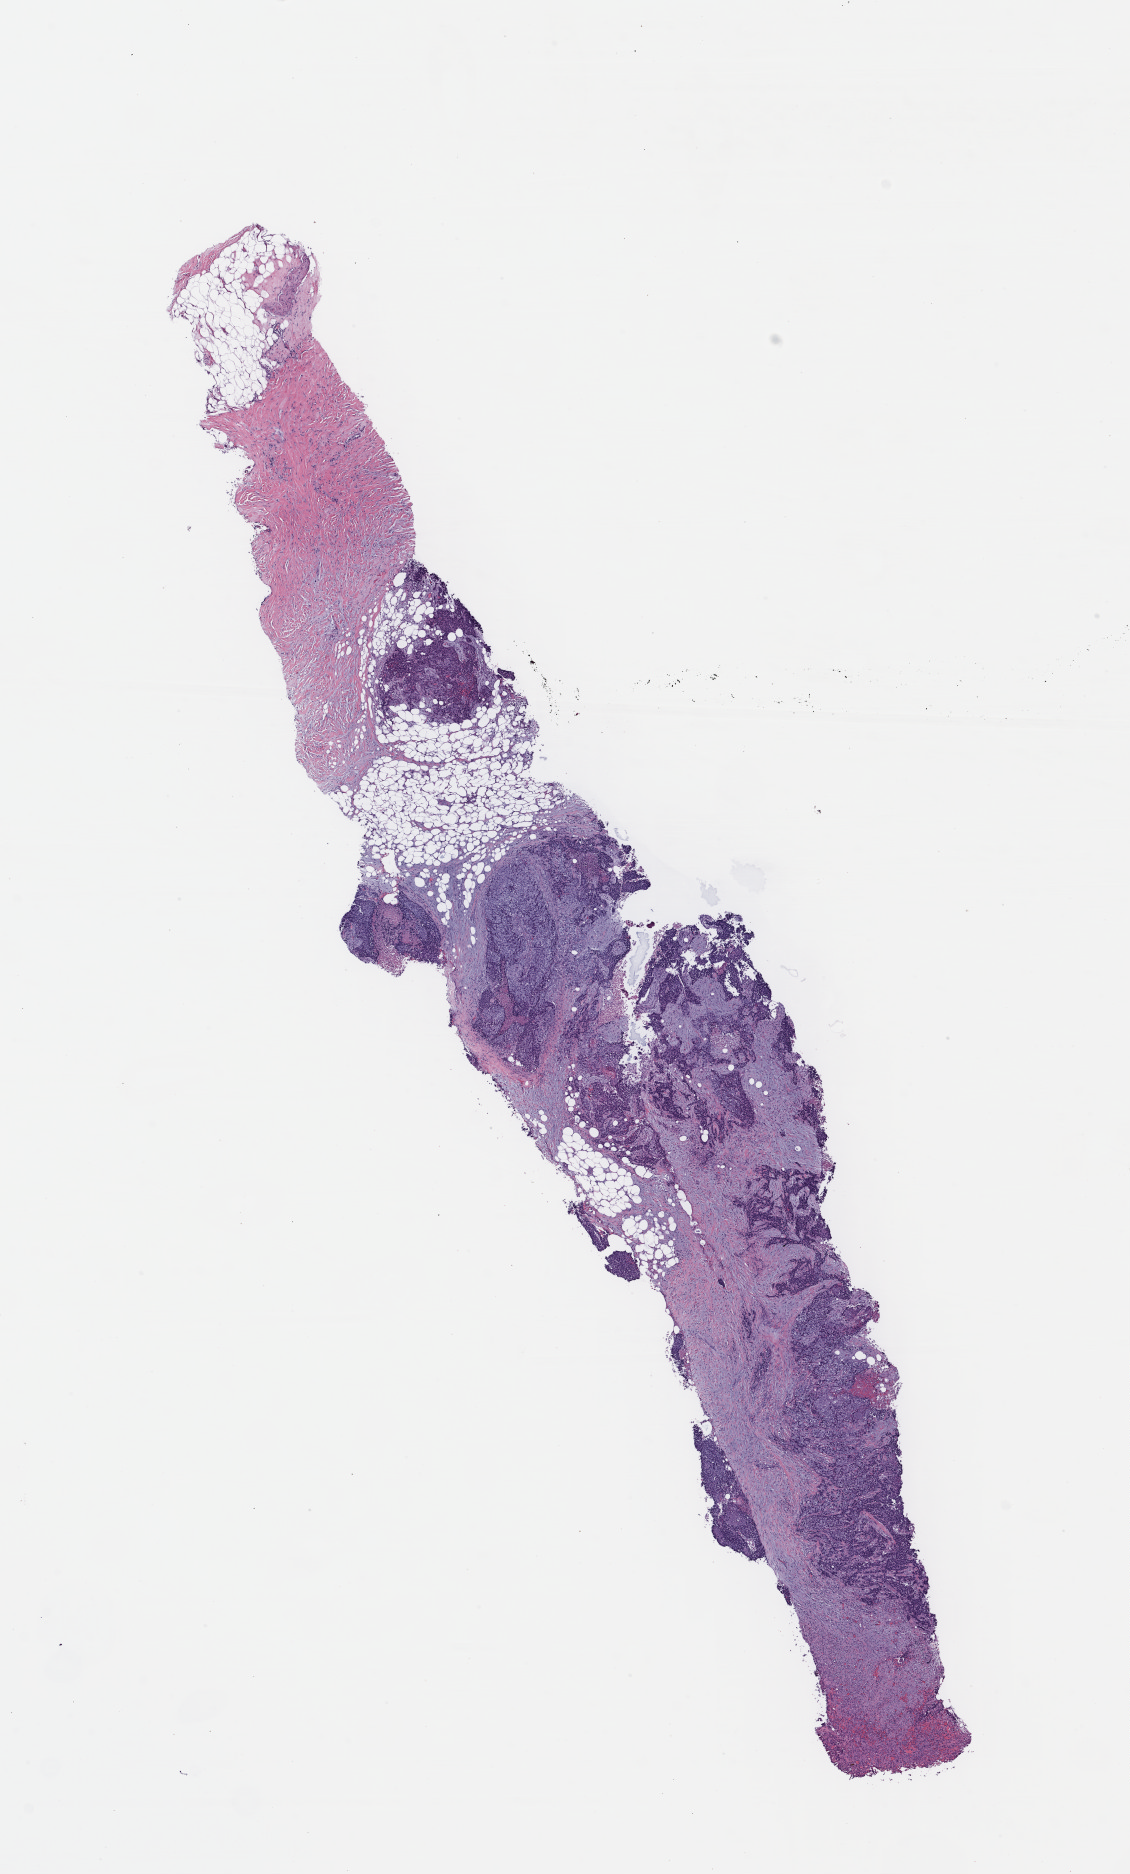
Hematoxylin and eosin (H&E) stained whole-slide image — shown as a low-resolution overview of the whole scanned area (about 8.9 x 14.7 mm). Formalin-fixed paraffin-embedded (FFPE) diagnostic section. Primary tumour sample from the bladder. Patient: male, age at initial diagnosis 62 years. Histologic grade: high grade.
Pathologic diagnosis: Transitional cell carcinoma. AJCC pathologic stage: III. Lymph nodes positive (case pathology): 0 of 8 examined.